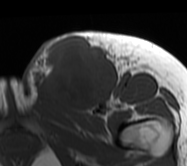
MRI of an extremity soft-tissue mass, one axial slice; position 28 of 62 along the scan axis; MR volume resampled by the dataset authors to the PET/CT grid (not the native acquisition matrix); 3.27 mm slice thickness; 187 × 166 image matrix. Female patient. From the clinical record (not read from this slice): histological type: leiomyosarcoma; grade: high; site of the primary tumour: groin.
Outlined on this slice (expert contour drawn on MRI and transferred to this co-registered scan by the dataset authors):
- gross tumour volume including surrounding oedema: bounding box (x1, y1, x2, y2) in pixels: (23, 30, 136, 116)
- gross tumour volume (mass): (32, 35, 117, 113)